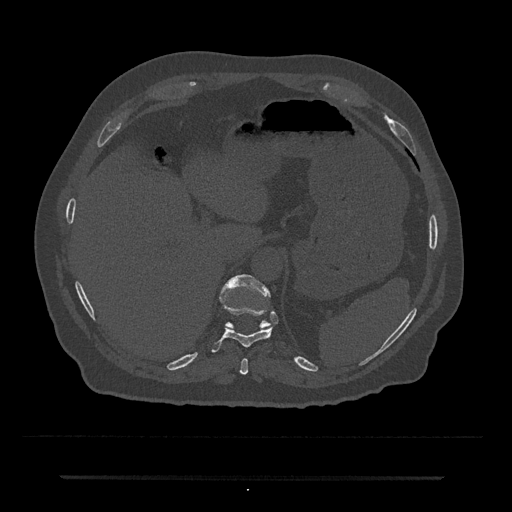
CT including the spine, one axial slice. Reconstruction kernel Br40s/3. 120 kVp. Bone window (W 1800 / L 400 HU). 0.5 mm slice thickness. 512 × 512 image matrix, field of view 437 × 437 mm. Male patient, age 69 years. Case-level facts recorded for this patient, not image findings: primary cancer: prostate.
Annotated regions visible in this slice (semi-automatically segmented with operator editing):
- T10 vertebra: bounding box (x1, y1, x2, y2) in pixels: (211, 305, 273, 353)
- T11 vertebra: (219, 274, 271, 329)
- T9 vertebra: (240, 358, 248, 375)